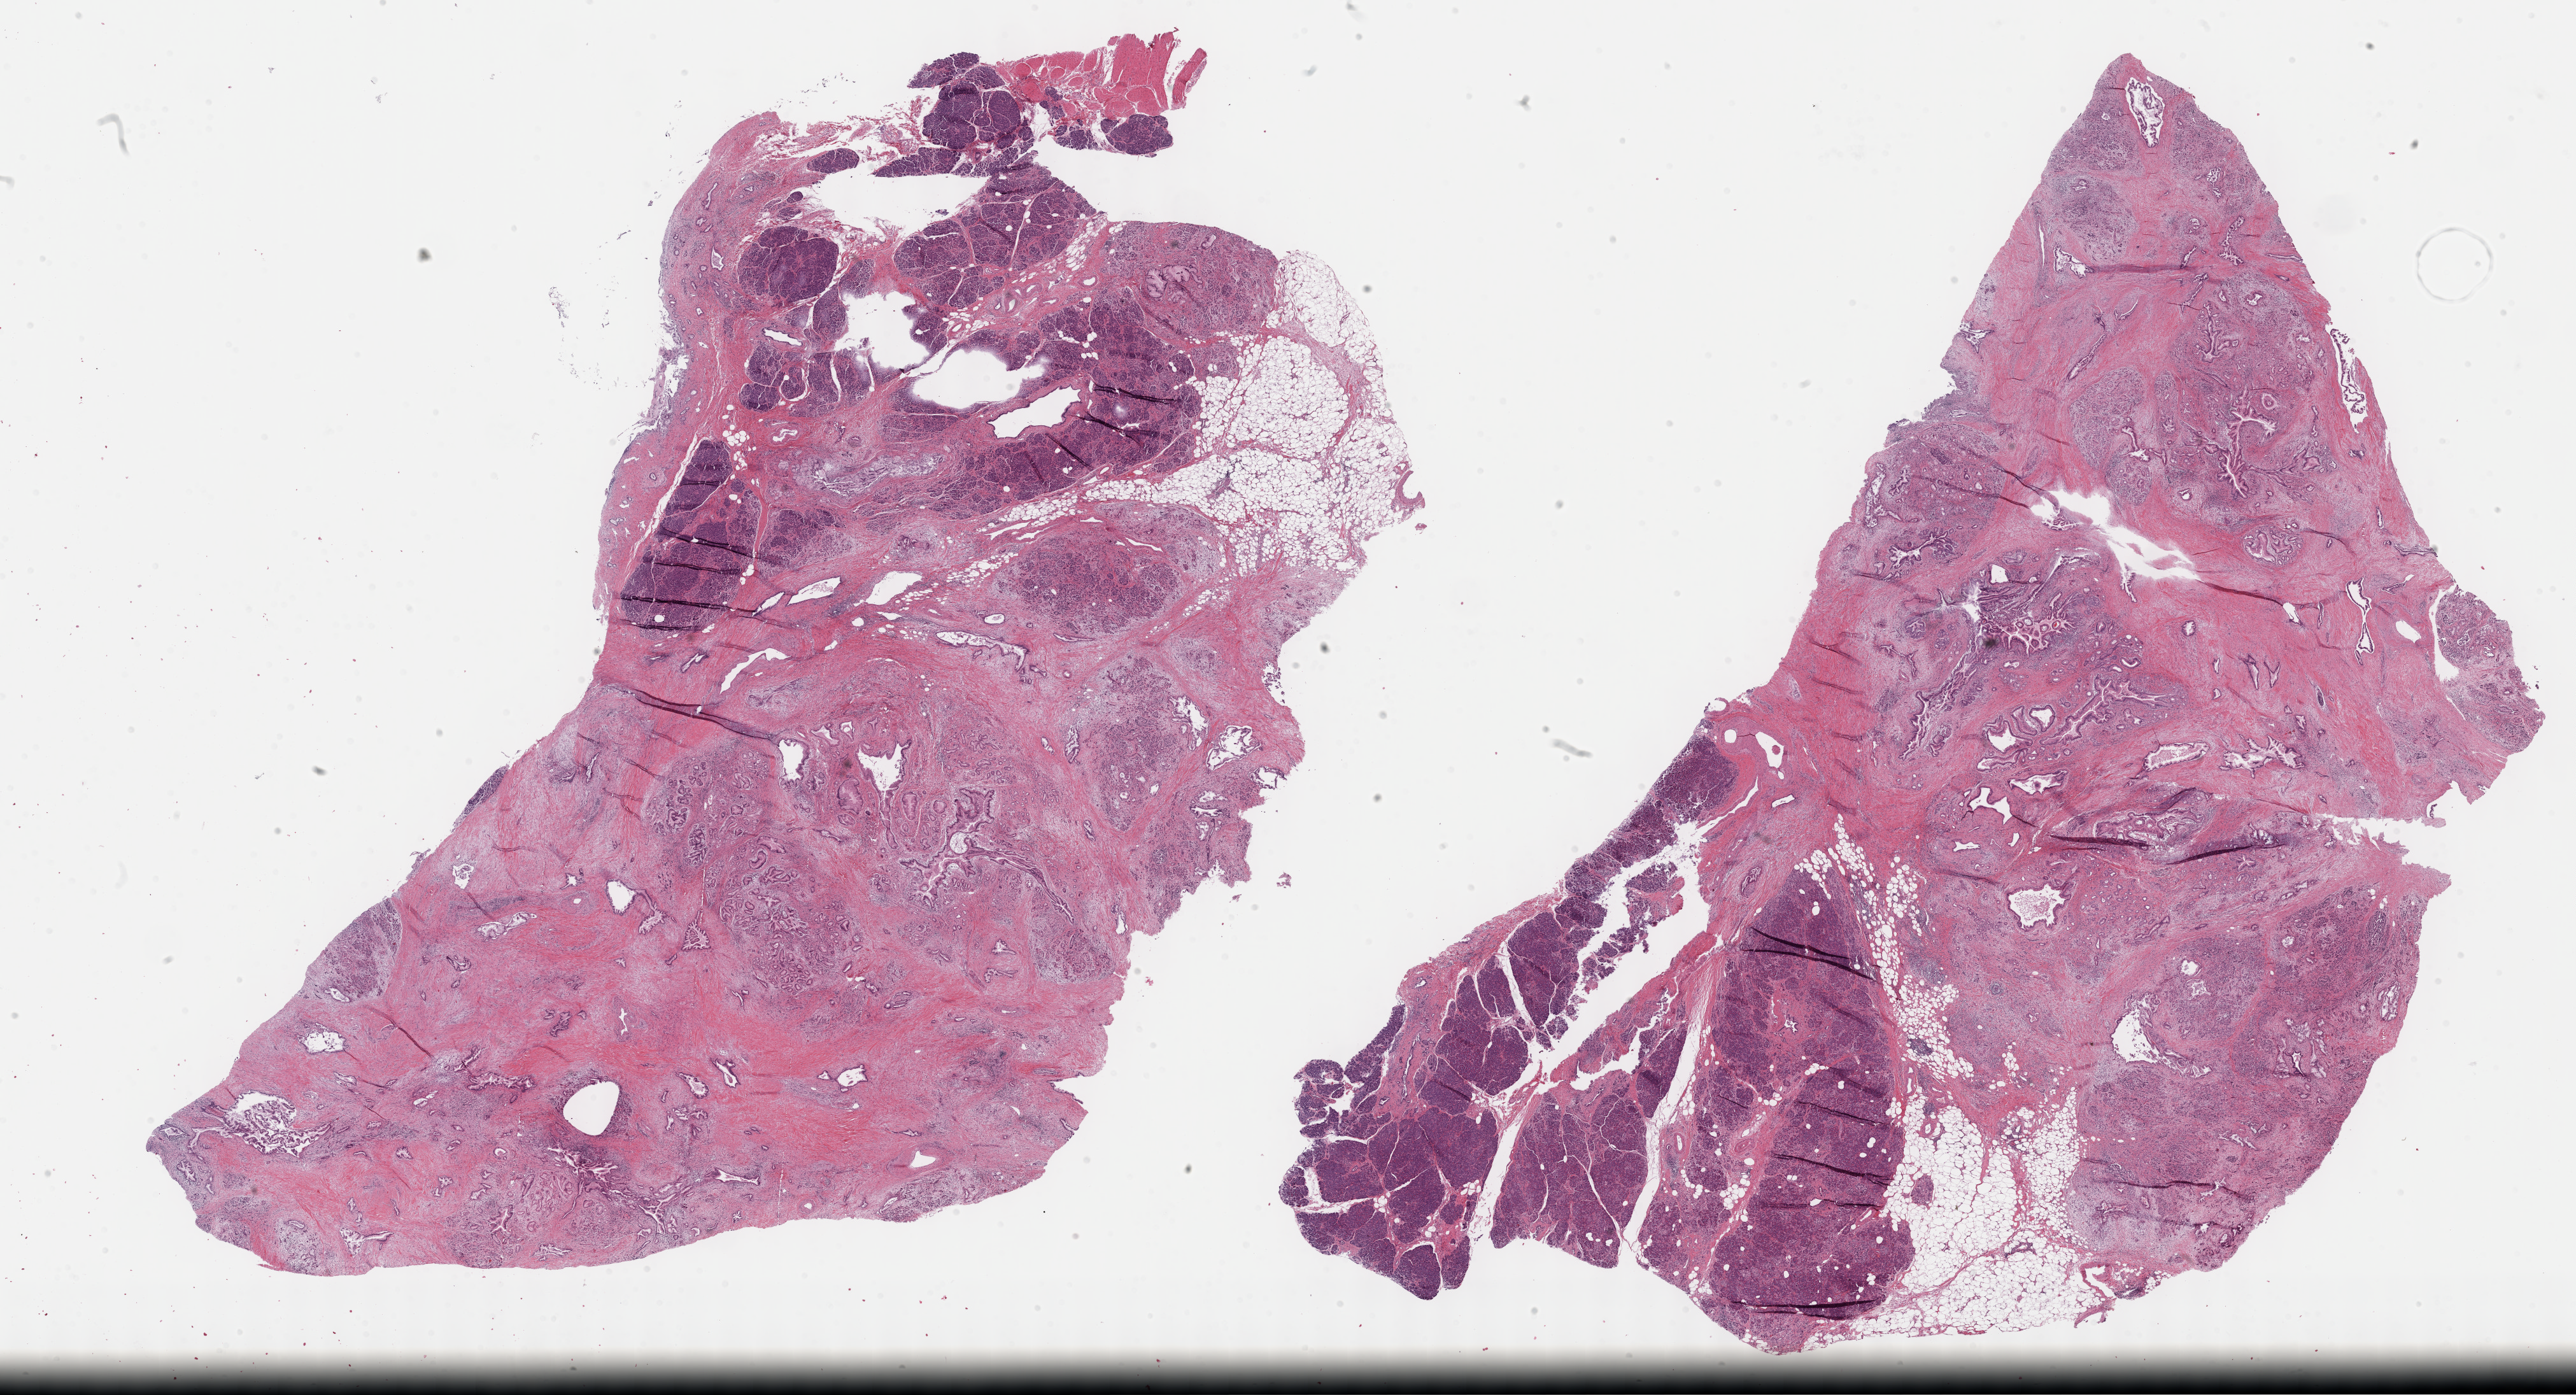
Hematoxylin and eosin (H&E) stained whole-slide image — shown as a low-resolution overview of the whole scanned area (about 32.7 x 17.7 mm, acquisition: 40x scan), formalin-fixed paraffin-embedded (FFPE) diagnostic section, sample: primary tumour, pancreas. Male patient; age at initial diagnosis 65 years. Histologic grade: G3 (poorly differentiated).
Lymph nodes positive (case pathology): 7 of 22 examined. AJCC pathologic stage: IIB (7th edition). Histologic diagnosis: Mucinous adenocarcinoma (head of pancreas).